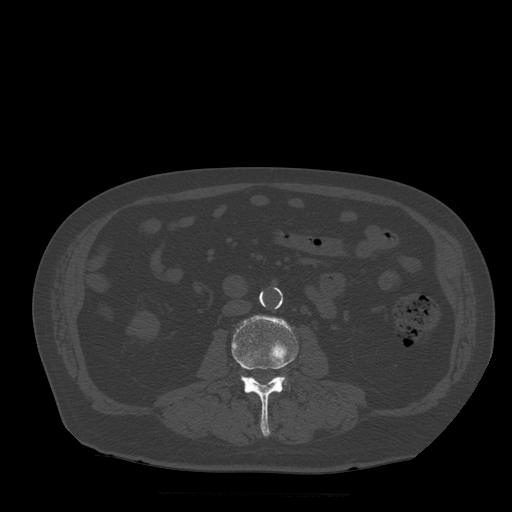
CT including the spine, one axial slice; slice 139 of 522 in the series (ordered by position); bone window (W 1800 / L 400 HU); 512 × 512 image matrix, field of view 420 × 420 mm. Patient age 72 years. From the clinical record (not read from this slice): primary cancer: prostate.
Outlined on this slice (semi-automatically segmented with operator editing):
- L3 vertebra: bounding box [x1, y1, x2, y2] px = [232, 316, 299, 436]
- L4 vertebra: [248, 377, 286, 385]